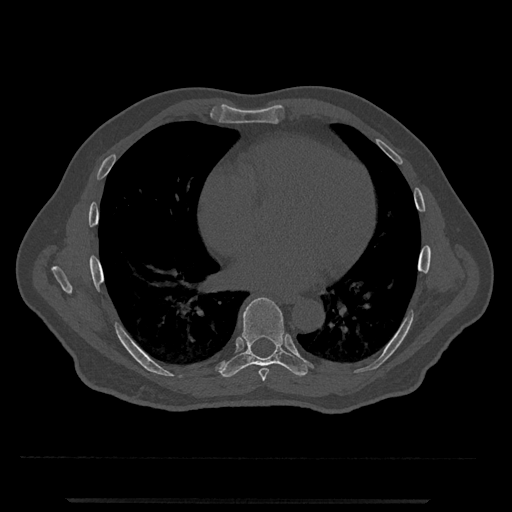
CT including the spine, one axial slice. Slice 642 of 797 in the series (ordered by position). Reconstruction kernel Br40s/3. Bone window (W 1800 / L 400 HU). 0.5 mm slice thickness. 512 × 512 image matrix, field of view 419 × 419 mm. Patient: male, 63 years. From the clinical record (not read from this slice): primary cancer: prostate.
Outlined on this slice (semi-automatically segmented with operator editing):
- T7 vertebra: bounding box [x1, y1, x2, y2] px = [259, 368, 269, 382]
- T8 vertebra: [220, 297, 313, 377]